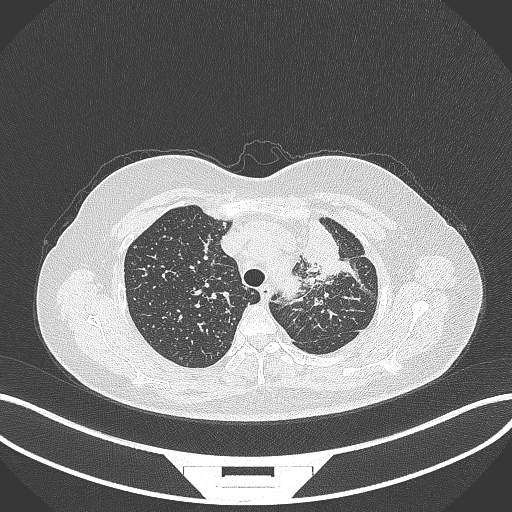
Chest CT, one axial slice; slice 261 of 348 in the series (ordered by position); reconstruction kernel B70f; lung window (W 1500 / L -600 HU); 512 × 512 image matrix. Female patient, age 49 years. From the clinical record (not read from this slice): clinical TNM (as recorded): T1c N0 M1.
Annotated regions visible in this slice (rectangle marked by the reading radiologist):
- lung tumour (recorded histology: adenocarcinoma): bounding box [x1, y1, x2, y2] px = [290, 215, 351, 282]